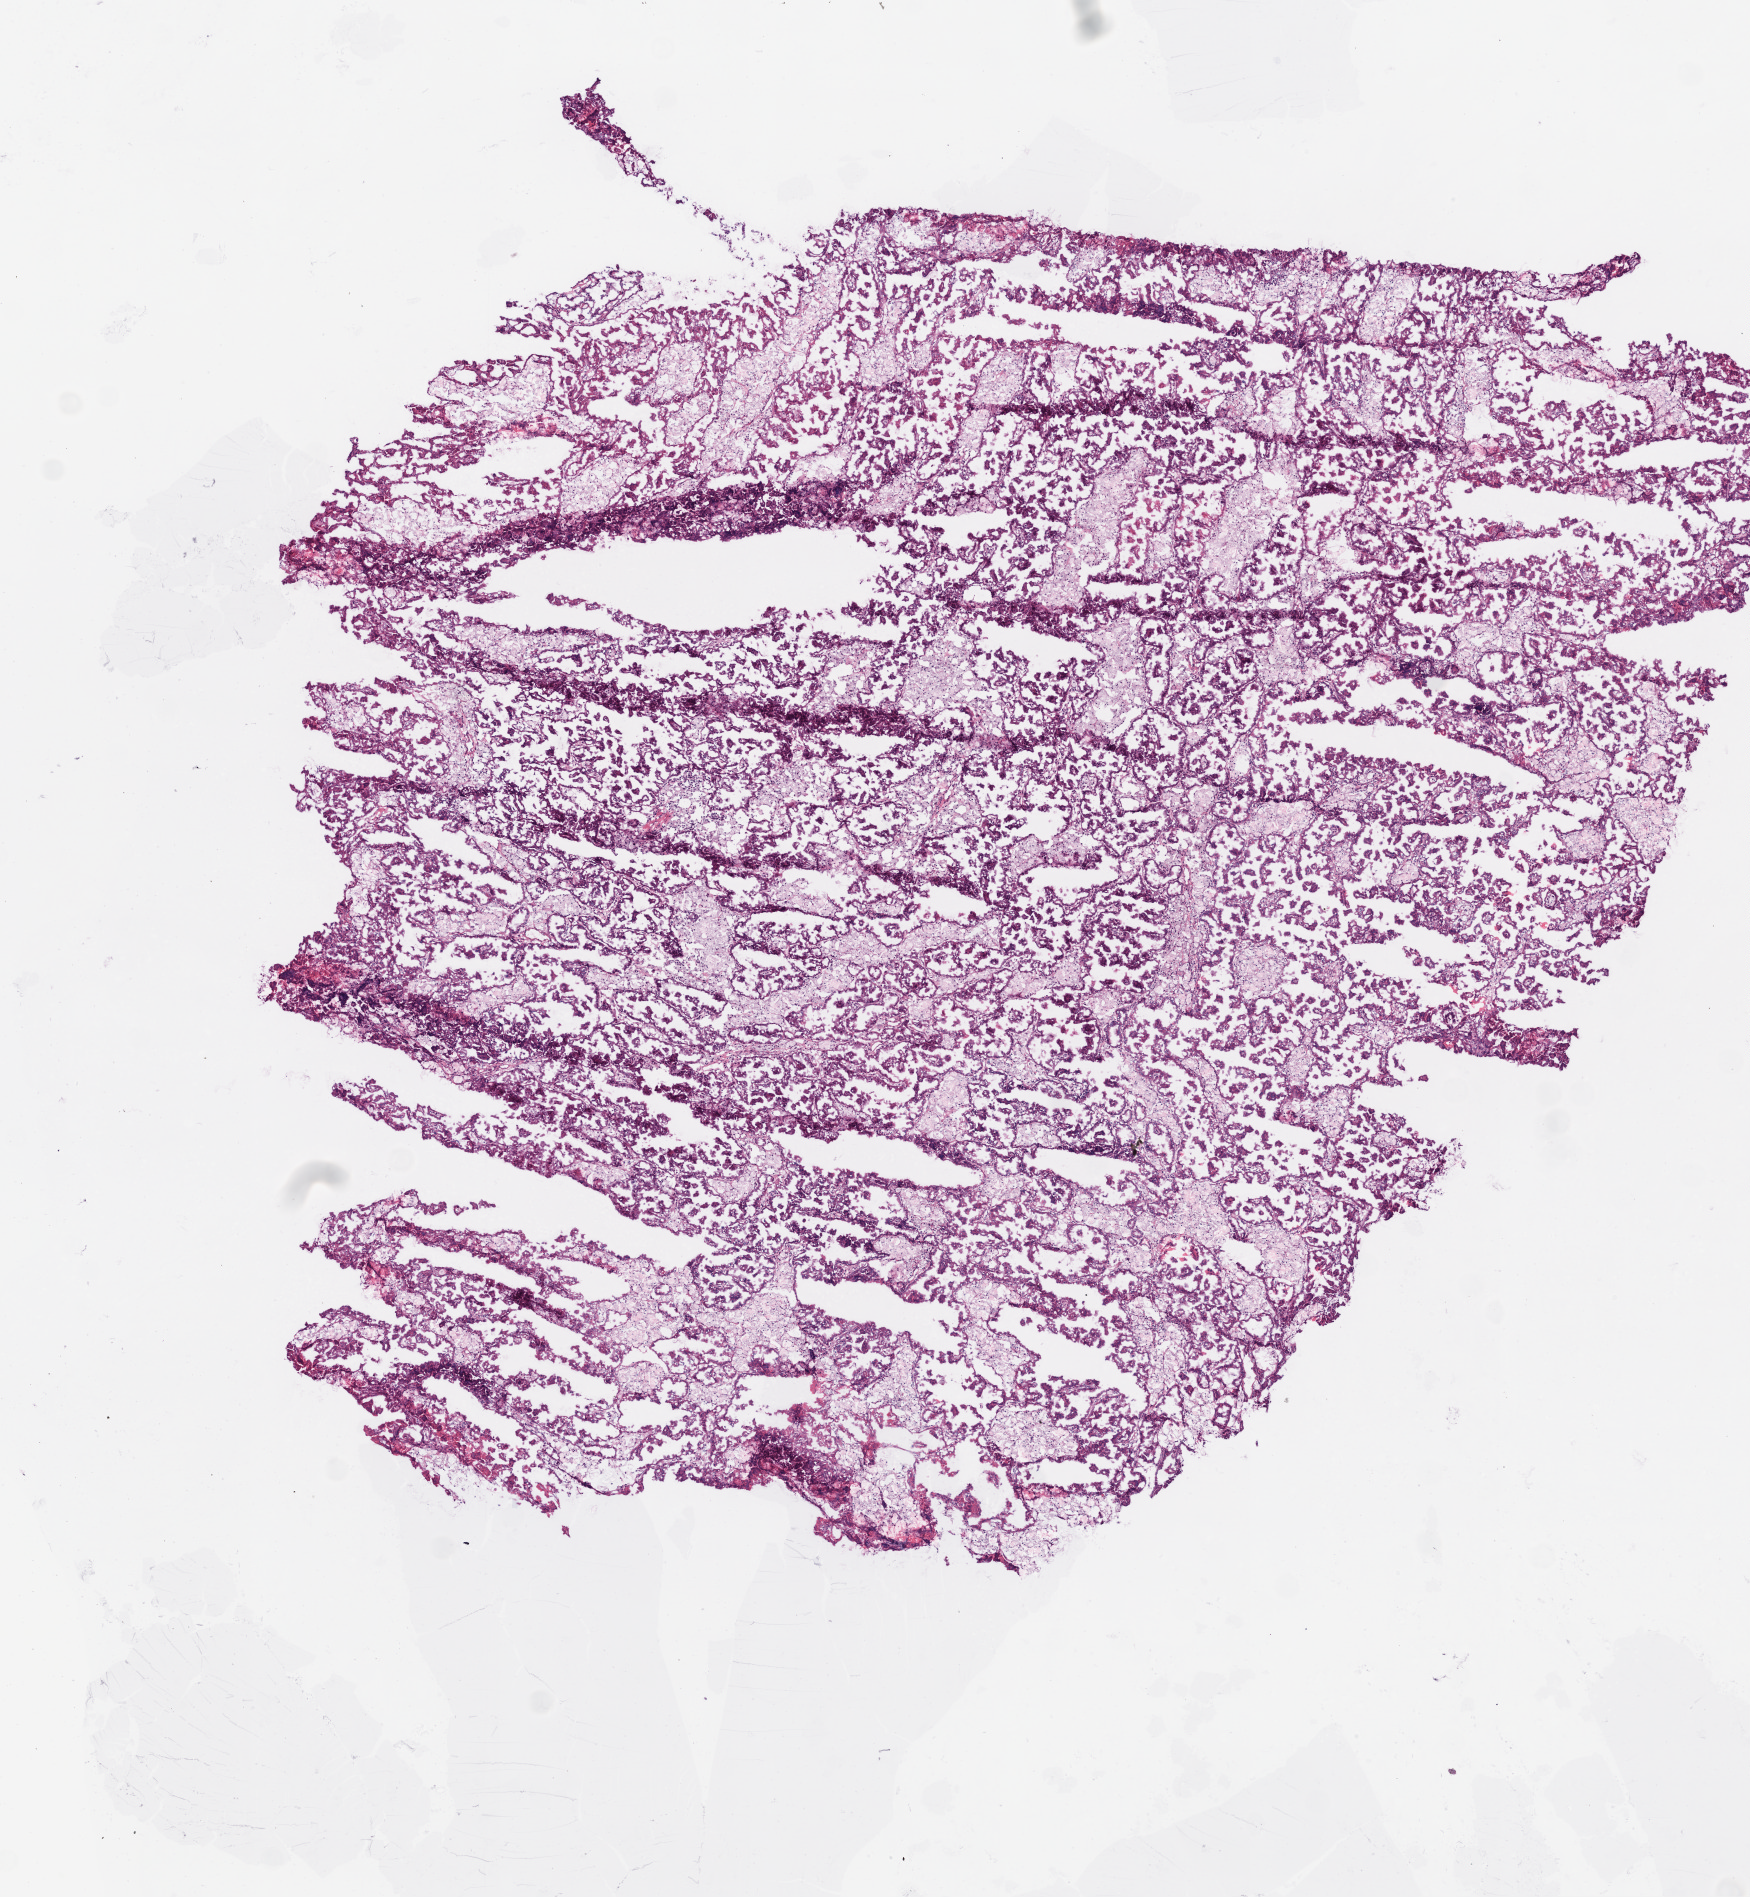
H&E-stained whole-slide image, low-resolution overview of the scanned area, about 7.0 x 7.6 mm (acquisition: 20x scan). Frozen section. Kidney, primary tumour sample. Patient: male, age at initial diagnosis 49 years. Pathologist review of this section (percent, as recorded): tumour cells 80%, tumour nuclei 75%, normal cells 0%, stromal cells 20%, necrosis 0%.
Laterality: left. Diagnosis: Papillary adenocarcinoma, NOS.